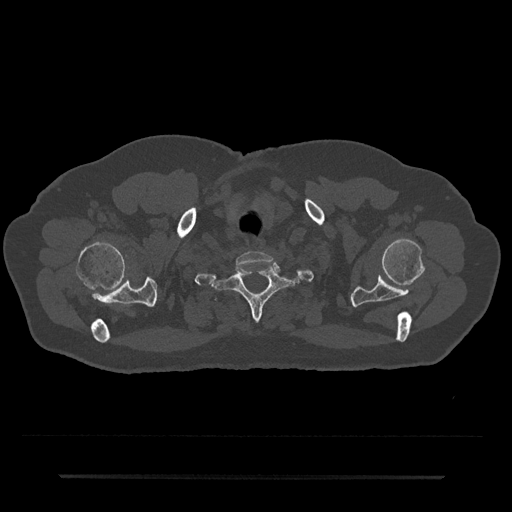
CT including the spine, one axial slice. Slice 643 of 797 in the series (ordered by position). 120 kVp. Bone window (W 1800 / L 400 HU). 512 × 512 image matrix. Patient: male, 69 years. From the clinical record (not read from this slice): primary cancer: prostate.
Structures marked on this image (semi-automatic segmentation, software-assisted and operator-edited):
- T1 vertebra: bounding box (x1, y1, x2, y2) in pixels: (212, 264, 301, 320)
- T2 vertebra: (215, 298, 217, 301)